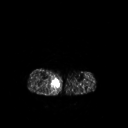
FDG PET of an extremity soft-tissue mass (from a PET/CT study), one axial slice. Position 127 of 267 along the scan axis. 3.27 mm slice thickness. 128 × 128 image matrix. Patient: male, 69 years. Case-level facts recorded for this patient, not image findings: histological type: pleiomorphic liposarcoma; grade: high; site of the primary tumour: right calf.
Structures marked on this image (expert contour drawn on MRI and transferred to this co-registered scan by the dataset authors):
- gross tumour volume including surrounding oedema: bounding box <51,76,60,94> (left, top, right, bottom; pixels)
- gross tumour volume (mass): <52,79,59,86>